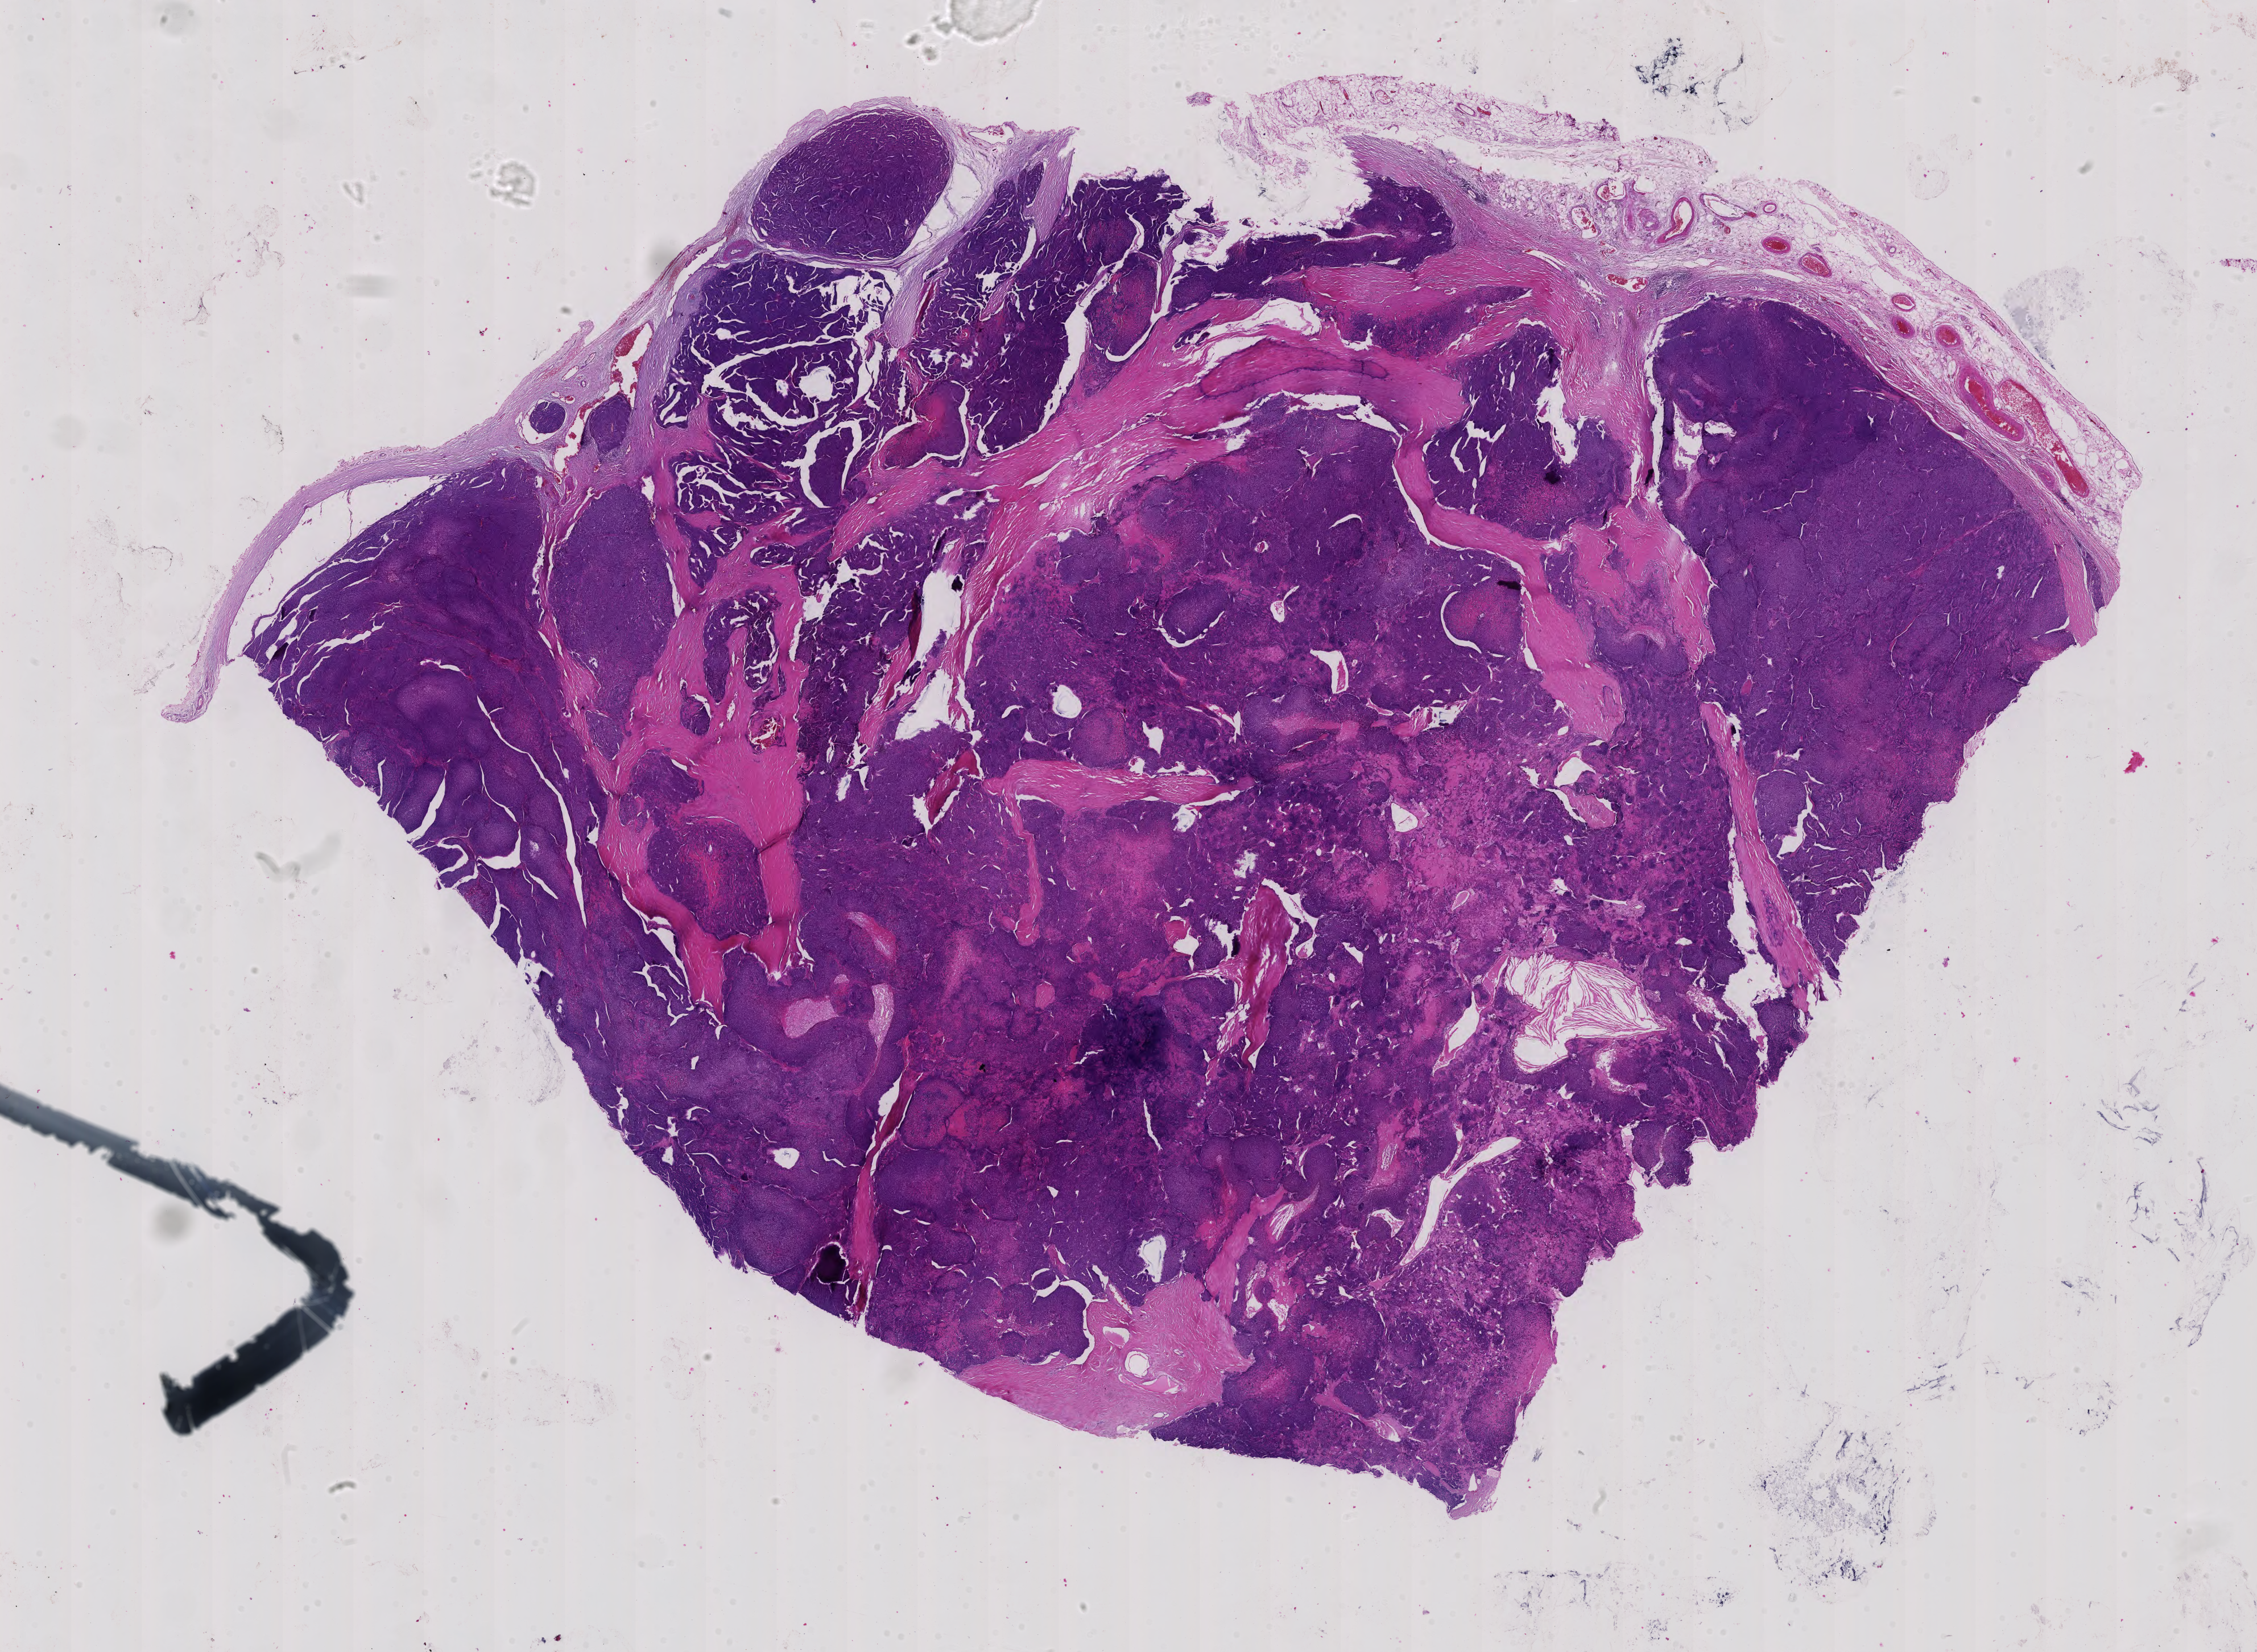
Digitized Hematoxylin and eosin (H&E) stained tissue section (whole slide) — shown as a low-resolution overview of the whole scanned area (about 28.9 x 21.2 mm). Formalin-fixed paraffin-embedded (FFPE) diagnostic section. Sample: primary tumour, thymus. Patient: male, age at initial diagnosis 64 years.
- diagnosis: Thymoma, type A, malignant